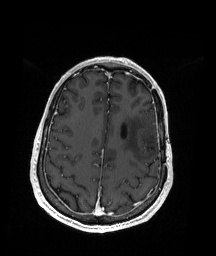
Brain MRI from a brain-tumour surgery series, one axial slice; position 59 of 192 along the scan axis; T1-weighted post-contrast; 1 mm slice thickness; 216 × 256 image matrix, field of view 211 × 250 mm. Case-level facts recorded for this patient, not image findings: histopathology: Oligodendroglioma; WHO grade: 2; IDH mutation: yes; tumour location: Left Insular.
Annotated regions visible in this slice (manually delineated by an expert):
- previous resection cavity: bounding box <147,127,159,137> (left, top, right, bottom; pixels)